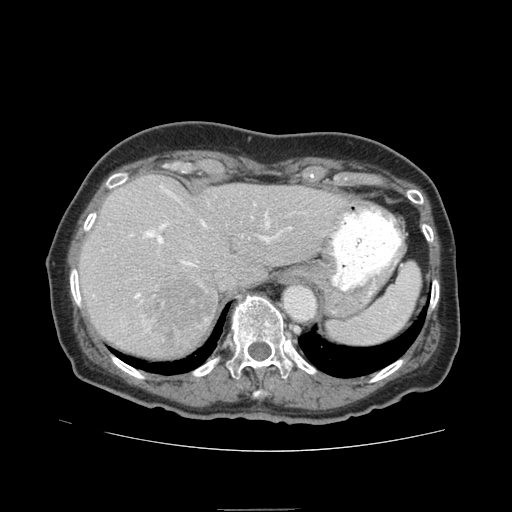
Contrast-enhanced abdominal CT (liver protocol), one axial slice; slice 62 of 95 in the series (ordered by position); reconstruction kernel STANDARD; 140 kVp; soft-tissue window (W 400 / L 40 HU); 2.5 mm slice thickness; 512 × 512 image matrix. Case-level facts recorded for this patient, not image findings: diagnosis: hepatocellular carcinoma (patient treated with transarterial chemoembolisation; whether this scan precedes or follows treatment is not stated here); TNM stage (as recorded): Stage-IVA; Child-Pugh class: B; tumour differentiation: moderately differentiated; tumour nodularity: uninodular.
Structures marked on this image (semi-automatically segmented with operator editing):
- liver parenchyma outside the tumour (the mass and vessels are separate outlines, so this box may not span the whole liver): bounding box <78,174,348,358> (left, top, right, bottom; pixels)
- mass: <135,275,213,351>
- liver vessels: <131,189,275,299>